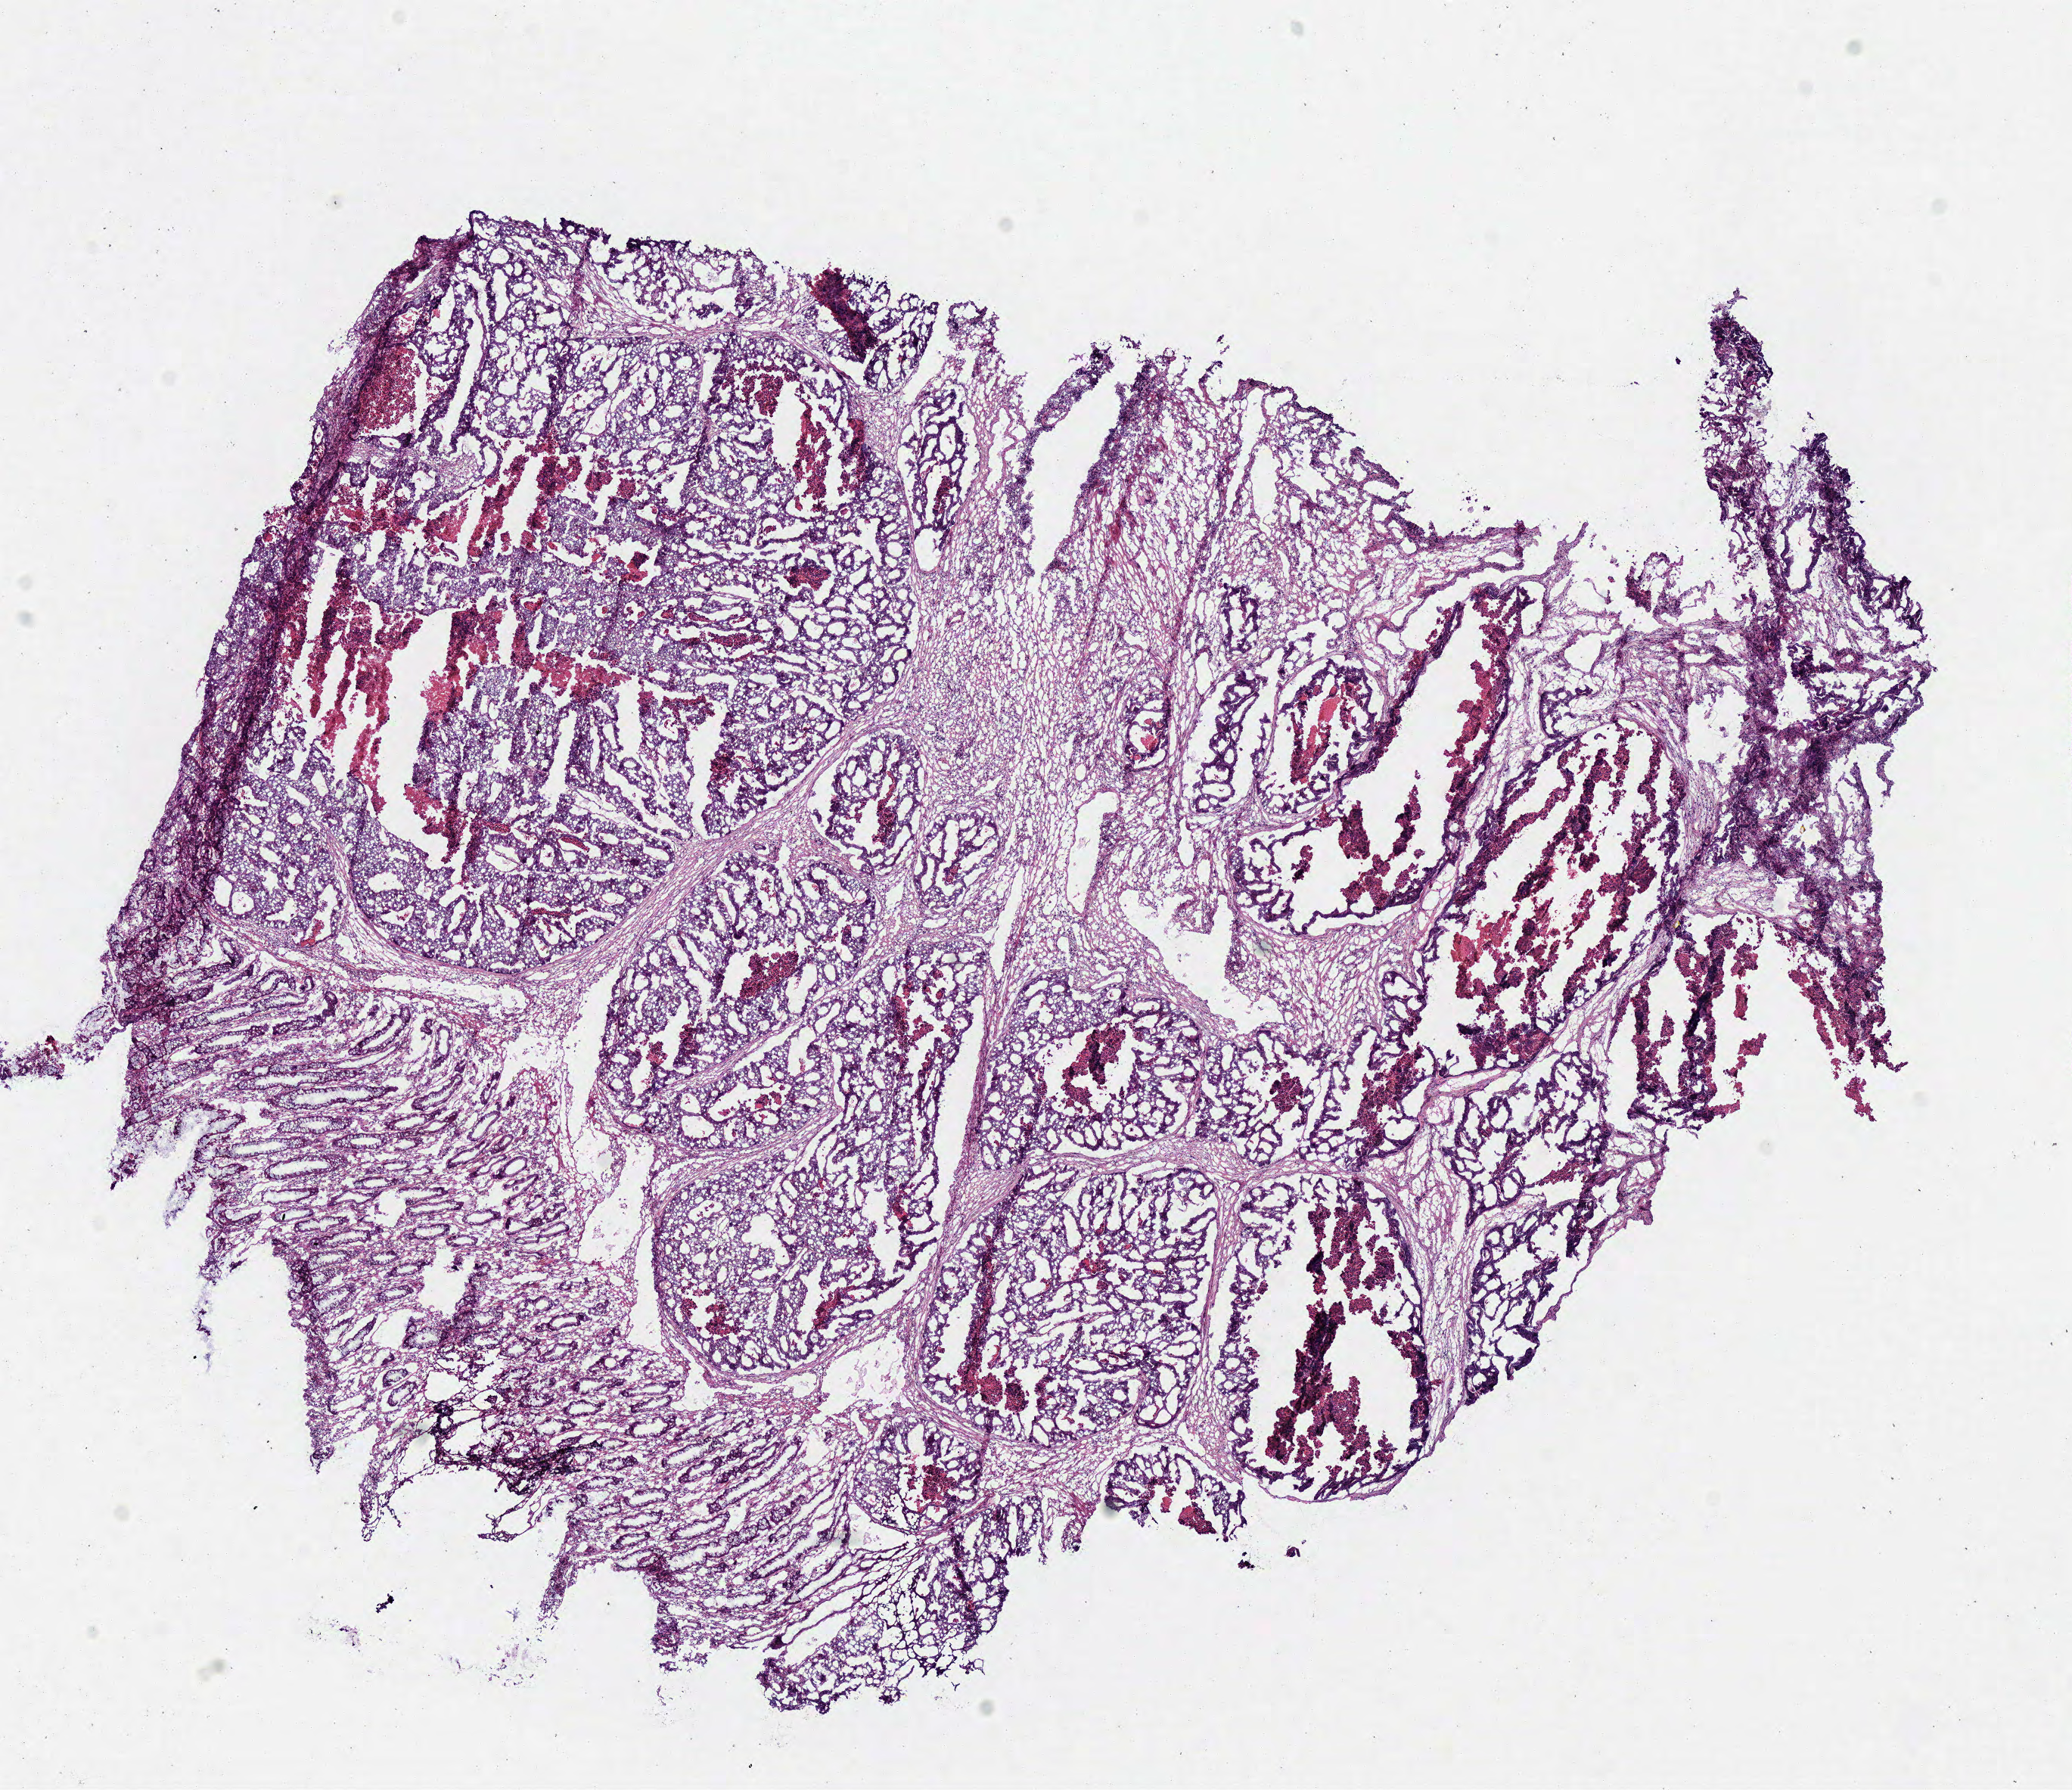
Whole-slide histology image, H&E-stained — shown as a low-resolution overview of the whole scanned area (about 10.8 x 9.3 mm, acquisition: 40x scan). Frozen section from the bottom of the tissue portion. Sample: primary tumour, colon. Patient: male, age at initial diagnosis 66 years.
Diagnosis: Adenocarcinoma, NOS (descending colon).